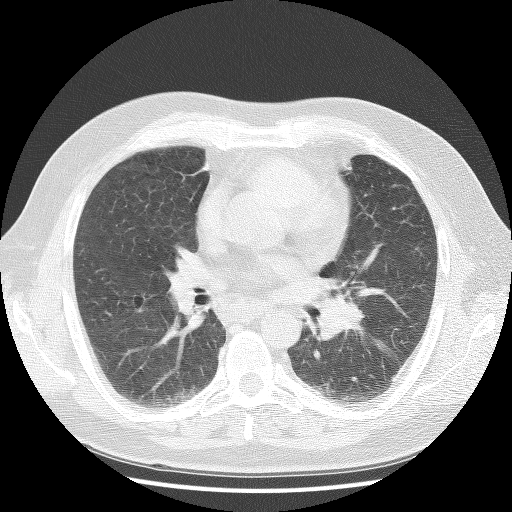
Chest CT (low-dose screening protocol), one axial image. First (baseline) screen. Lung window (W 1500 / L -600 HU). Lung (sharp) reconstruction kernel (BONE). 512 × 512 image matrix. Male participant, aged 59 years at enrolment. Current smoker at enrolment.
• Expert reader's lesion annotation, box from (x=302, y=287) to (x=378, y=362) px.
• Screening reader's record for this exam (one nodule recorded; not confirmed to be the boxed lesion): non-calcified nodule or mass ≥4 mm, right upper lobe, 4 × 4 mm, soft tissue attenuation.
• Note: the box lies in the patient's left hemithorax on this image, whereas the reader's record names the right lung; they may be different findings.
• Participant outcome: lung cancer diagnosed 20 days after this screen — non-small cell carcinoma, left hilum, stage IV (AJCC 6th edition).